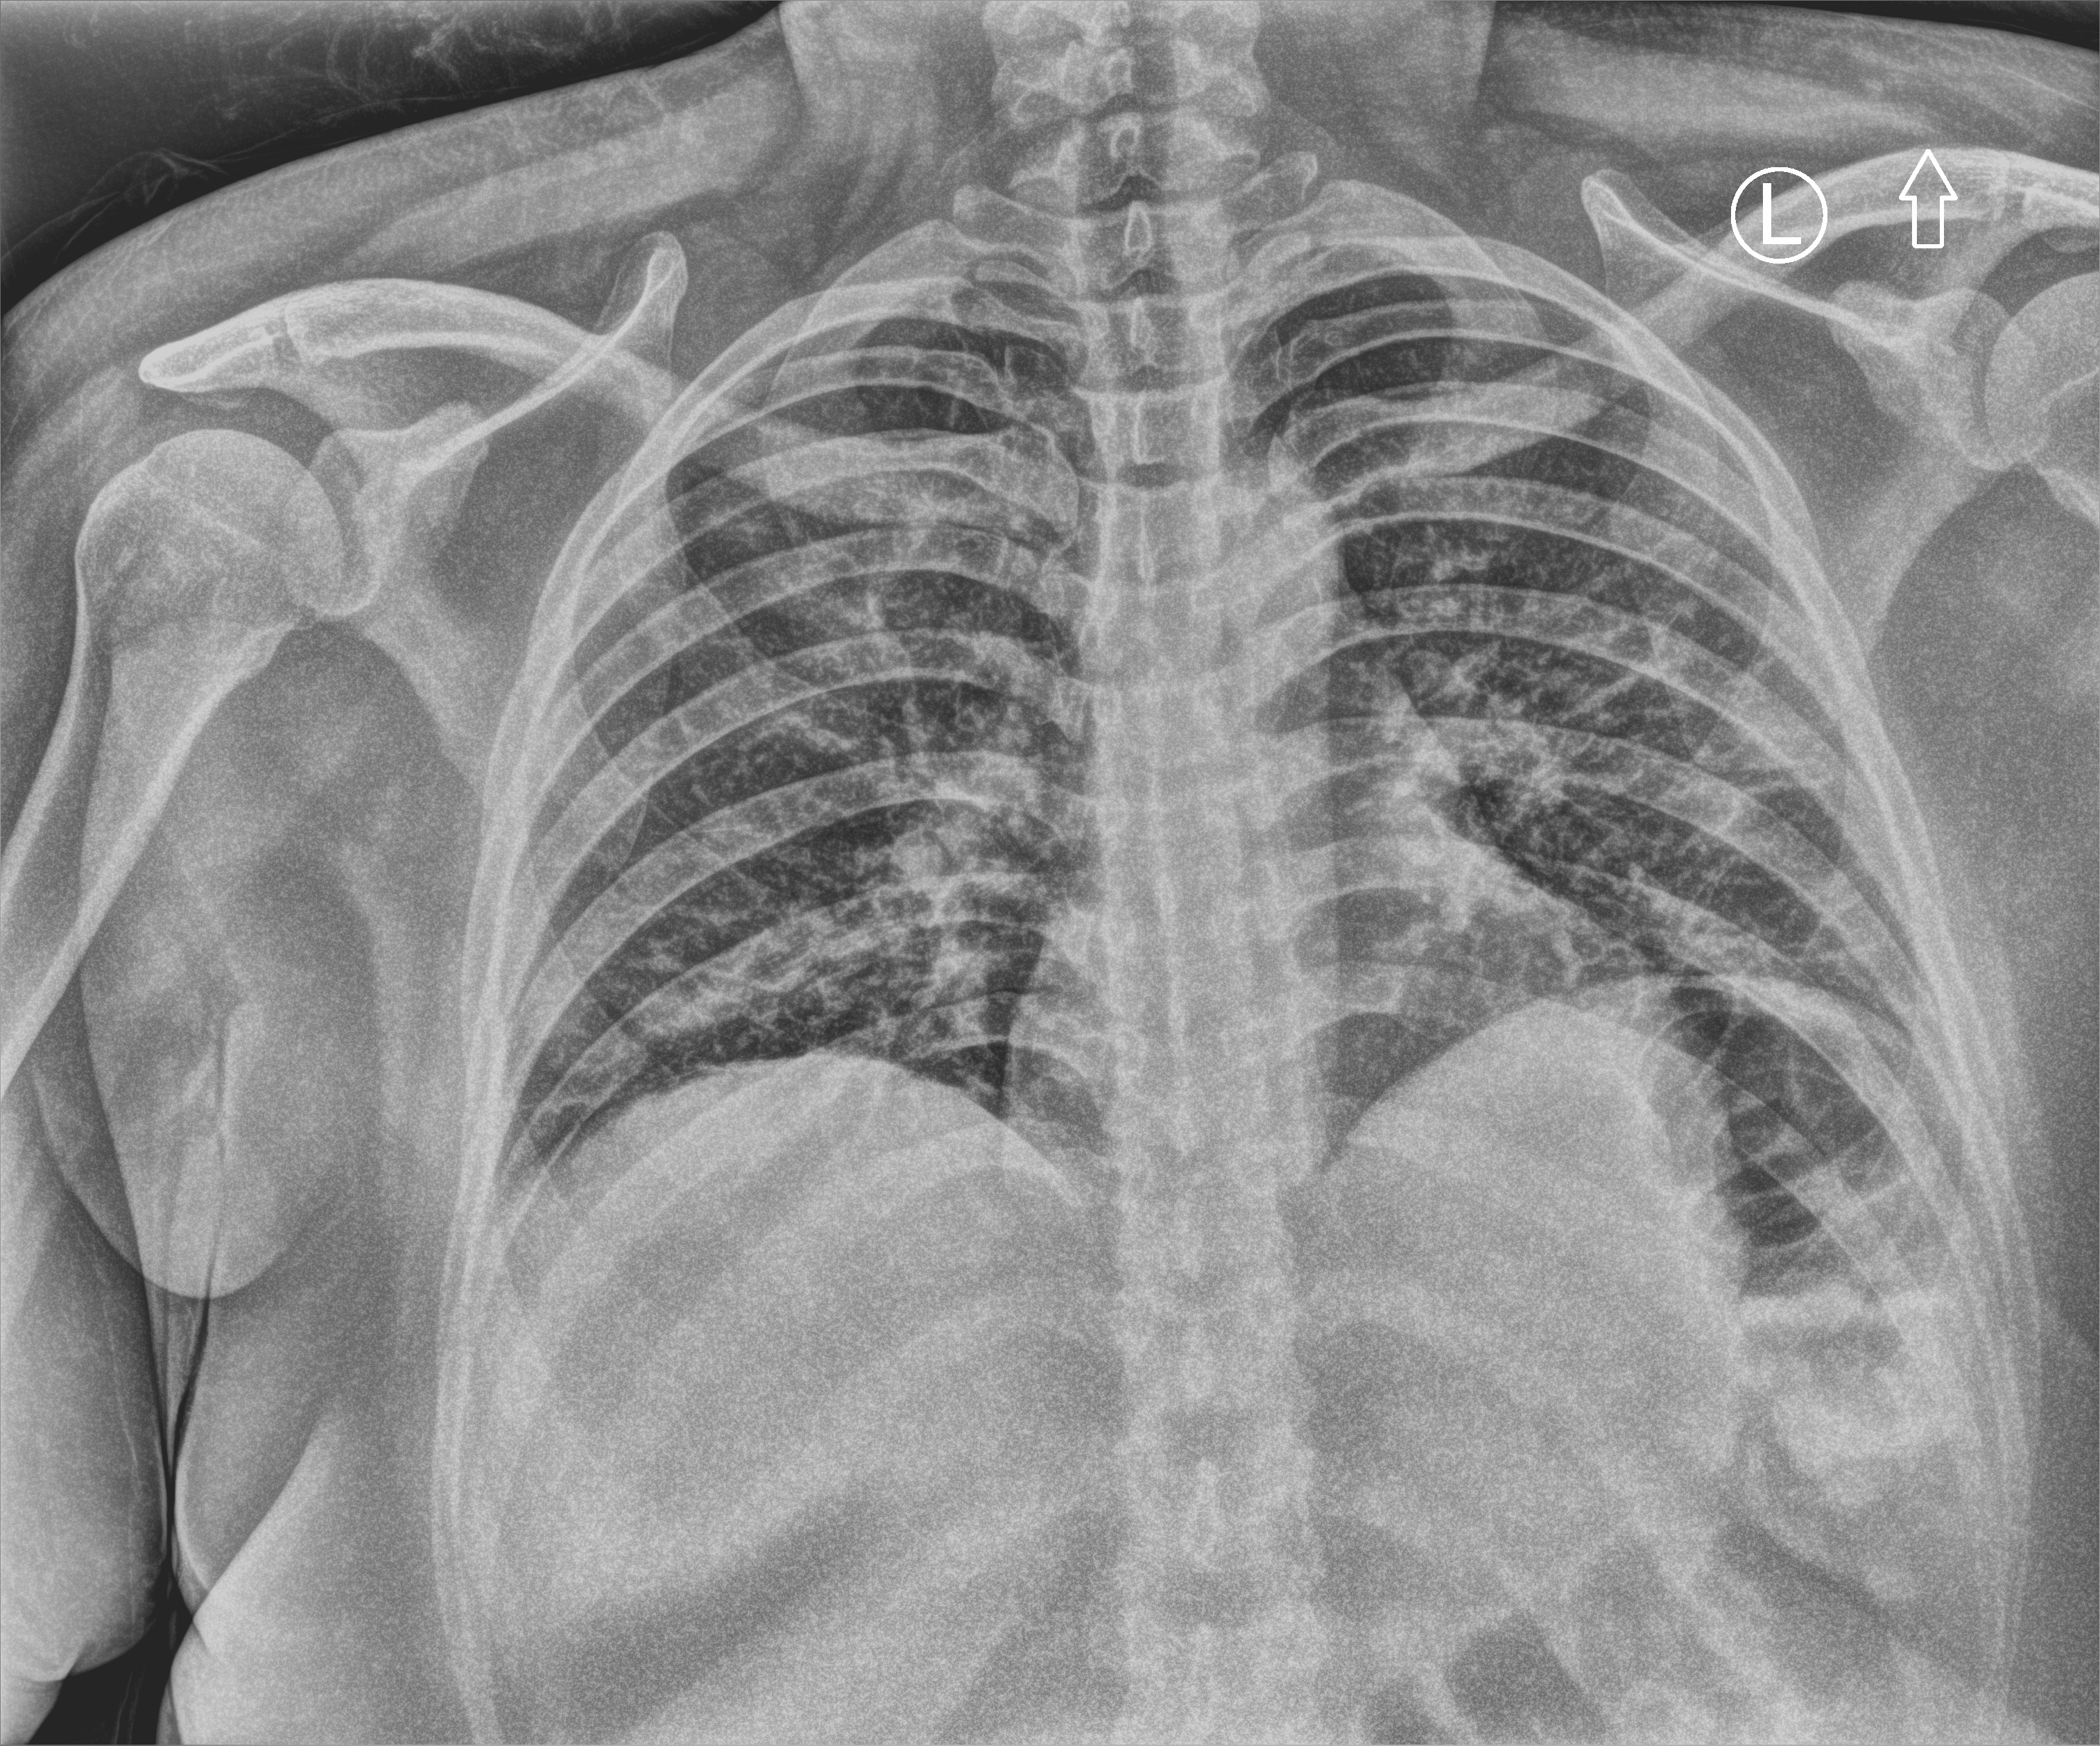
Chest X-ray (portable), anteroposterior (AP) projection. Patient hospitalised with COVID-19; female, aged 18–59 years.
From the hospital-stay record, not from the radiograph (when in the stay this image was taken is not recorded):
- admitted to intensive care during this hospital stay: no